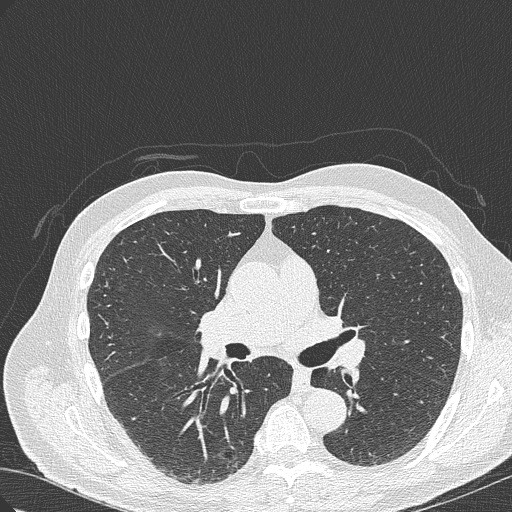
Axial slice from a low-dose chest CT screening exam, first (baseline) screen, lung window (W 1500 / L -600 HU), lung (sharp) reconstruction kernel (B50f), slice 135 of 322 in the series. Male participant, aged 70 years at enrolment.
Expert reader's lesion annotation, bounding box <199,419,262,475> (left, top, right, bottom; pixels). The screening reader recorded 4 non-calcified nodules or masses ≥4 mm on this exam (right lower lobe, right lower lobe, right upper lobe, right lower lobe); which of them this box marks is not recorded. Lung cancer was diagnosed 978 days after this screen (after the third annual screen): bronchiolo-alveolar adenocarcinoma, NOS, right lower lobe, poorly differentiated (G3), stage IB (AJCC 6th edition), 30 mm at pathology.